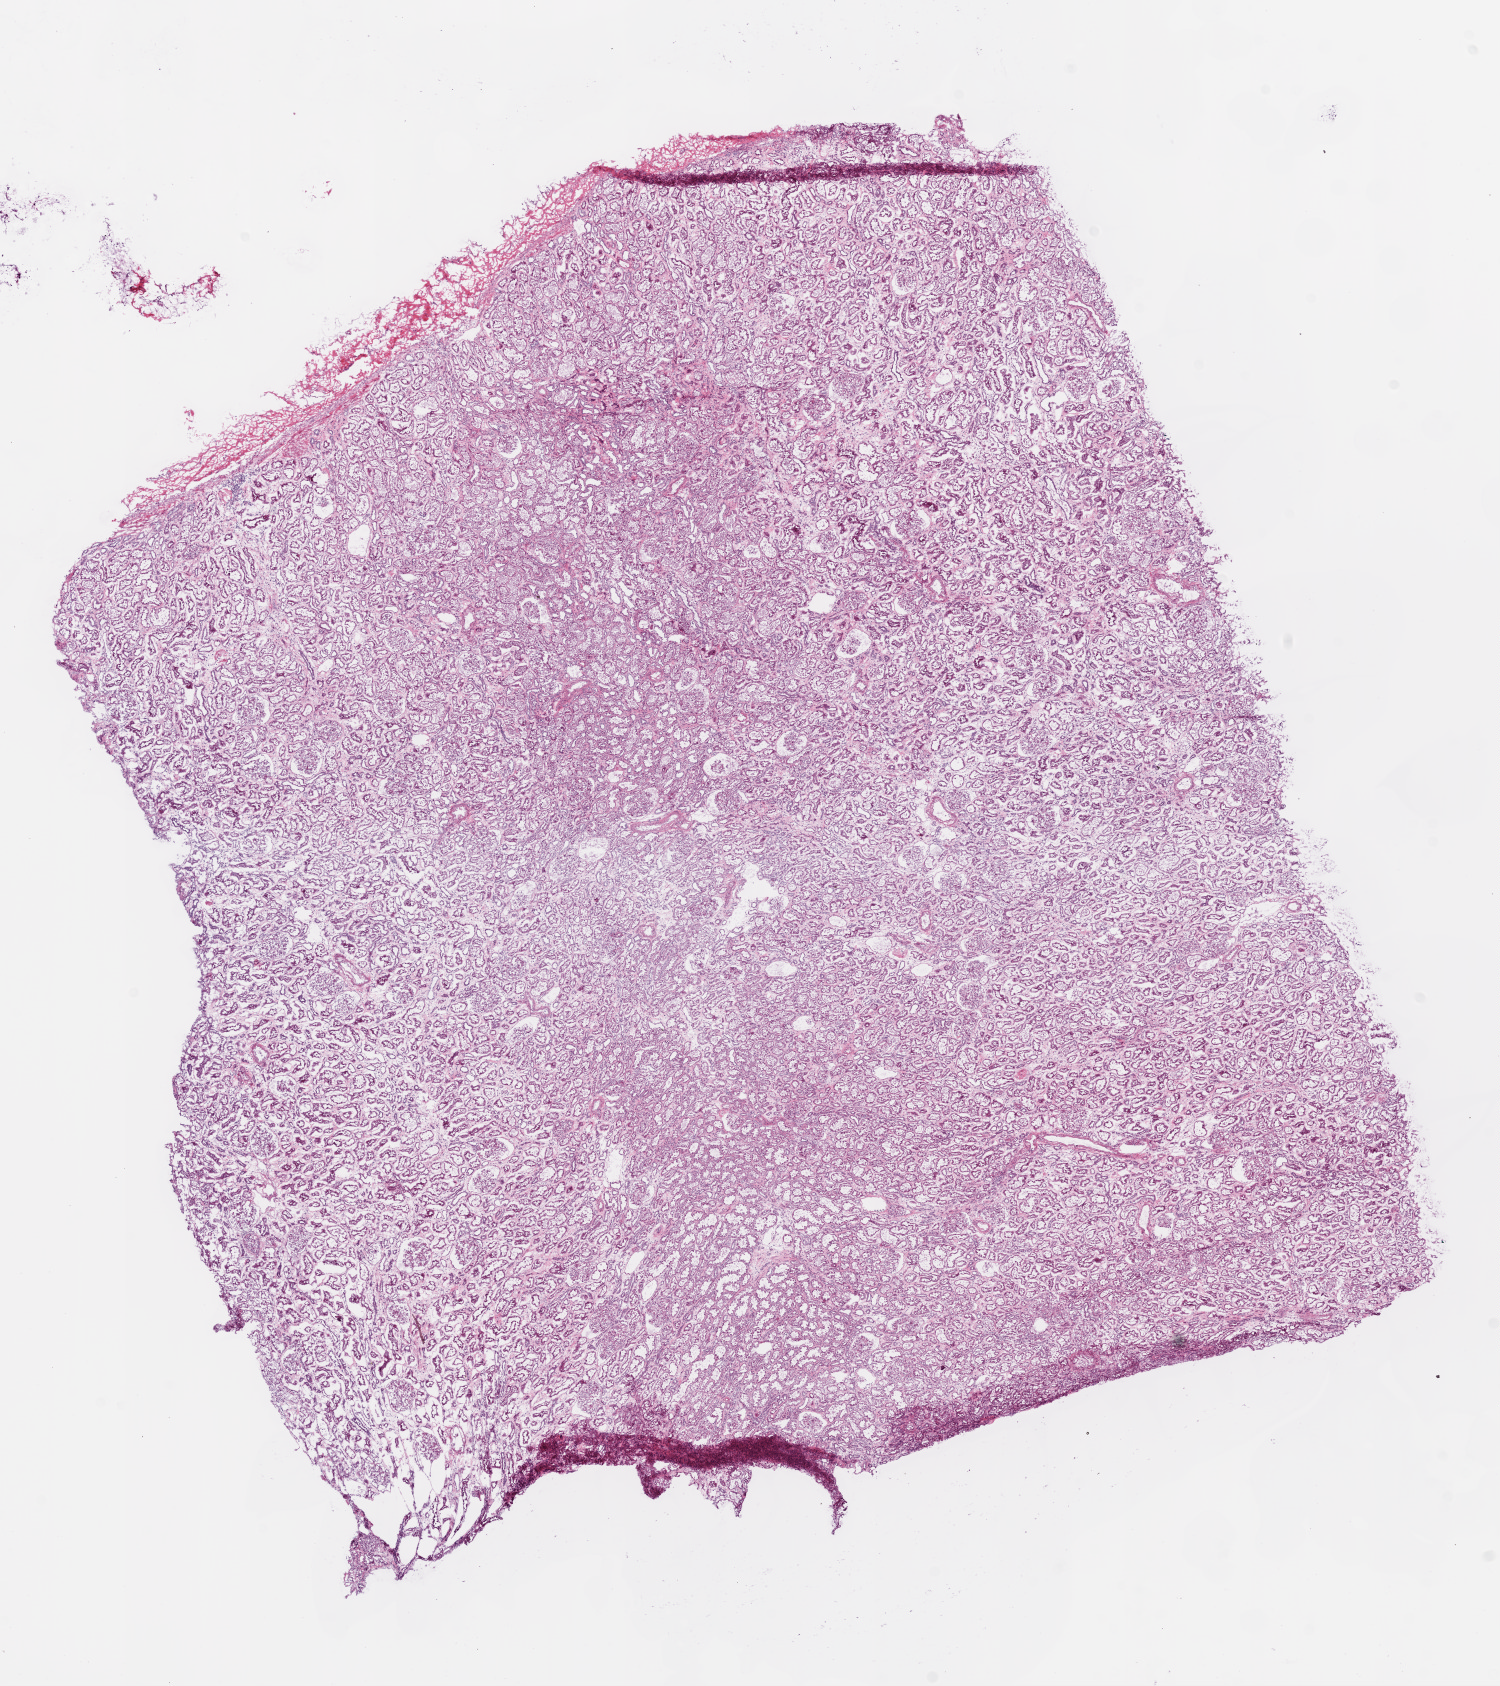
Digitized H&E-stained tissue section (whole slide), shown as a low-resolution overview of the whole scanned area (about 12.0 x 13.5 mm, from a 20x scan). Frozen section. Sample: solid tissue normal (non-tumour tissue), kidney. Patient: male, age at initial diagnosis 52 years.
* this section: solid tissue normal (non-tumour) sample from the same patient
* patient diagnosis: Clear cell adenocarcinoma, NOS